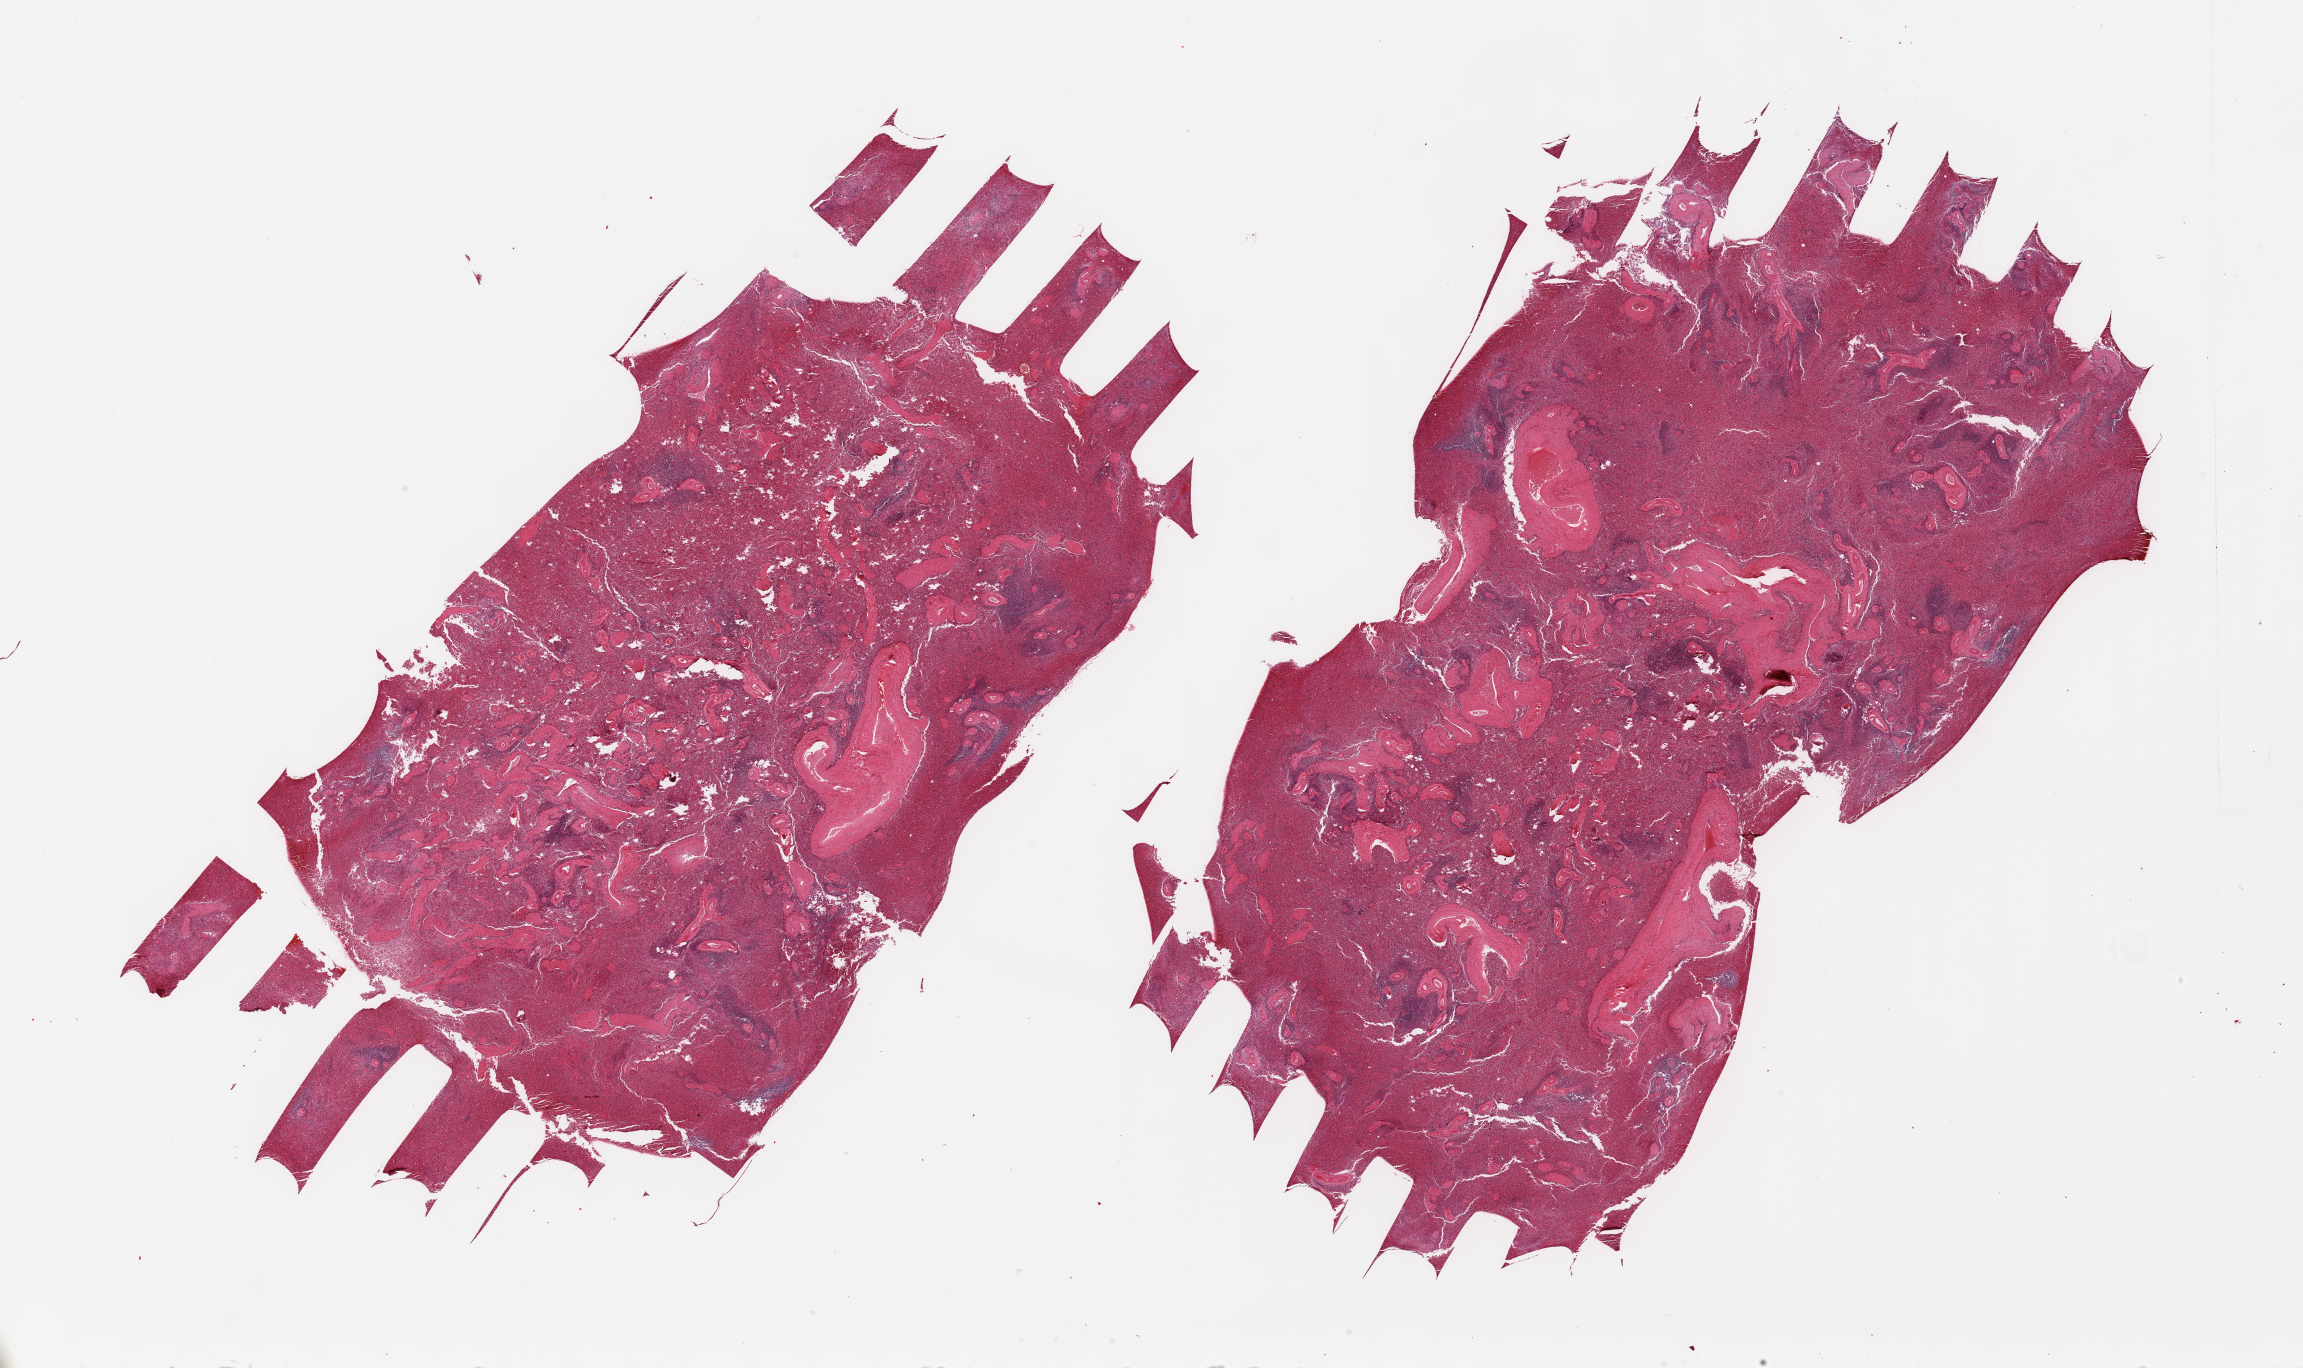
Haematoxylin and eosin whole-slide image — a low-resolution overview of the entire scanned area, about 36.4 x 21.6 mm. PAXgene-fixed, paraffin-embedded tissue. Section of spleen (target tissue). Donor tissue sample. Donor: male.
Review note (as recorded): 2 pieces, moderate congestion; evidence of remoted splenitis with fibrous scarring.